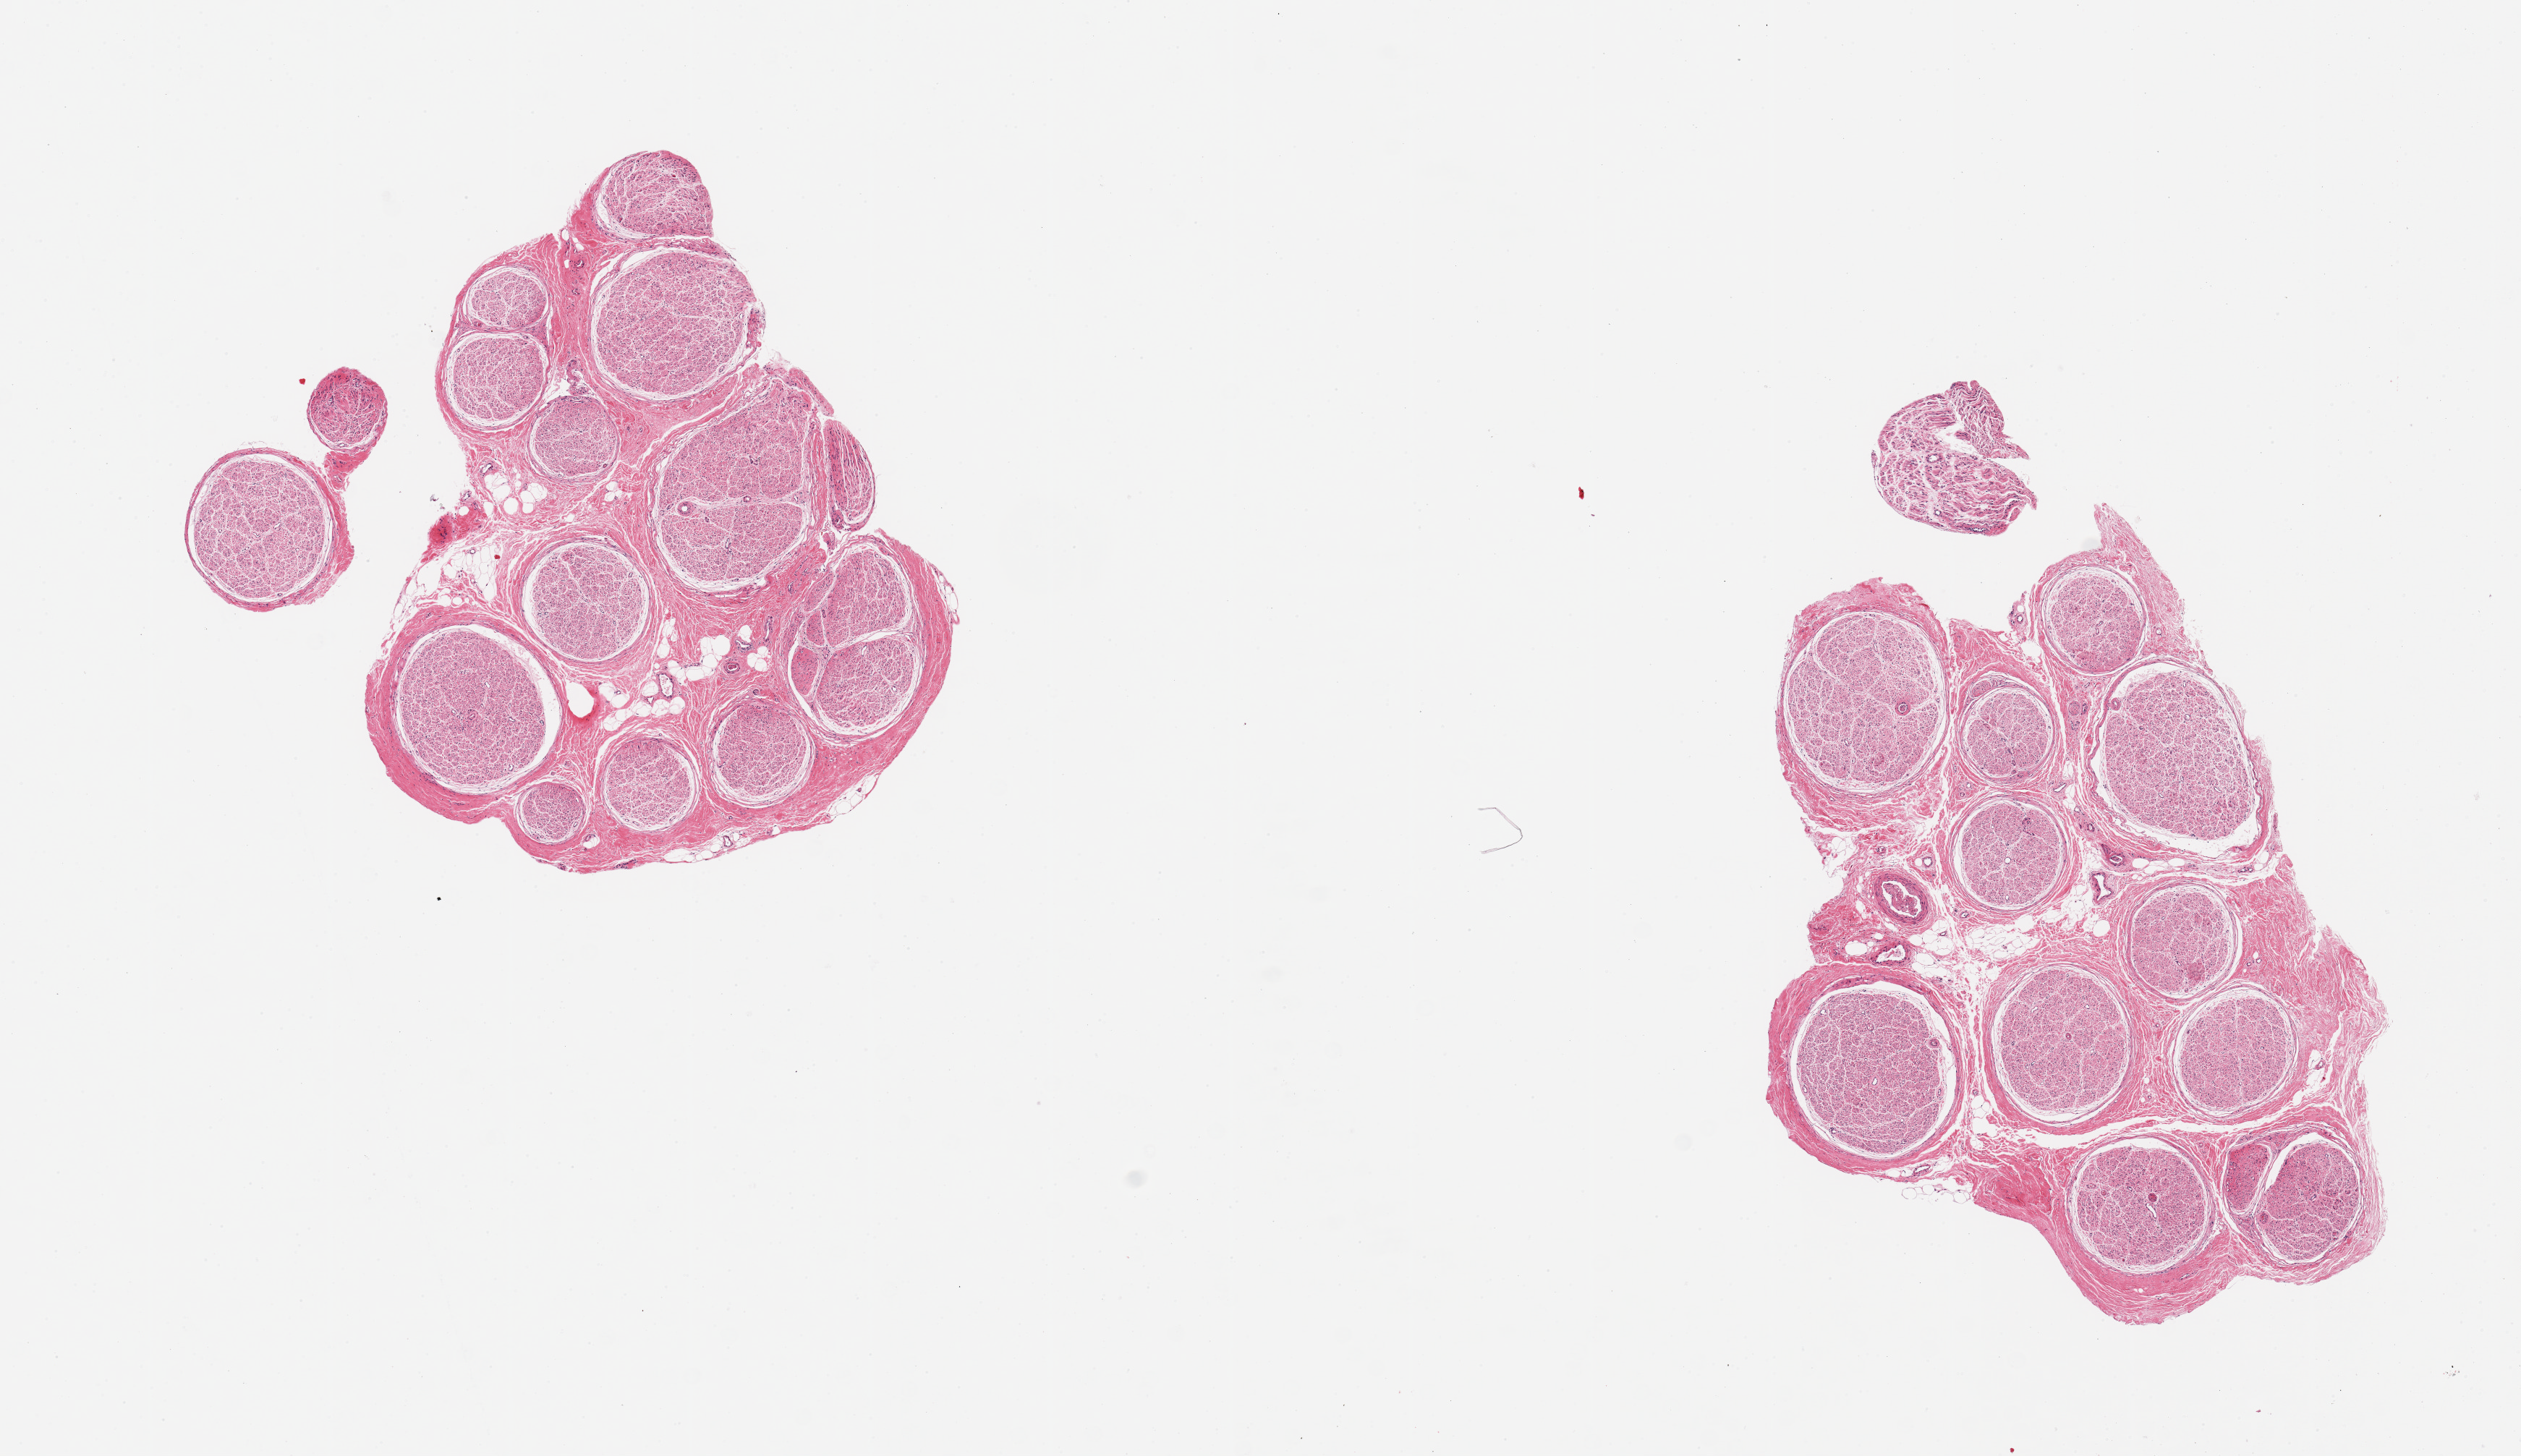
Digitized haematoxylin and eosin-stained section, brightfield — low-resolution overview of the scanned area, about 13.8 x 8.0 mm (from a 20x scan); PAXgene-fixed paraffin-embedded (PFPE) section; section of tibial nerve (target tissue); donor tissue sample. Donor sex: male.
• review note (as recorded): 2 pieces, good clean specimens; no adherent fat